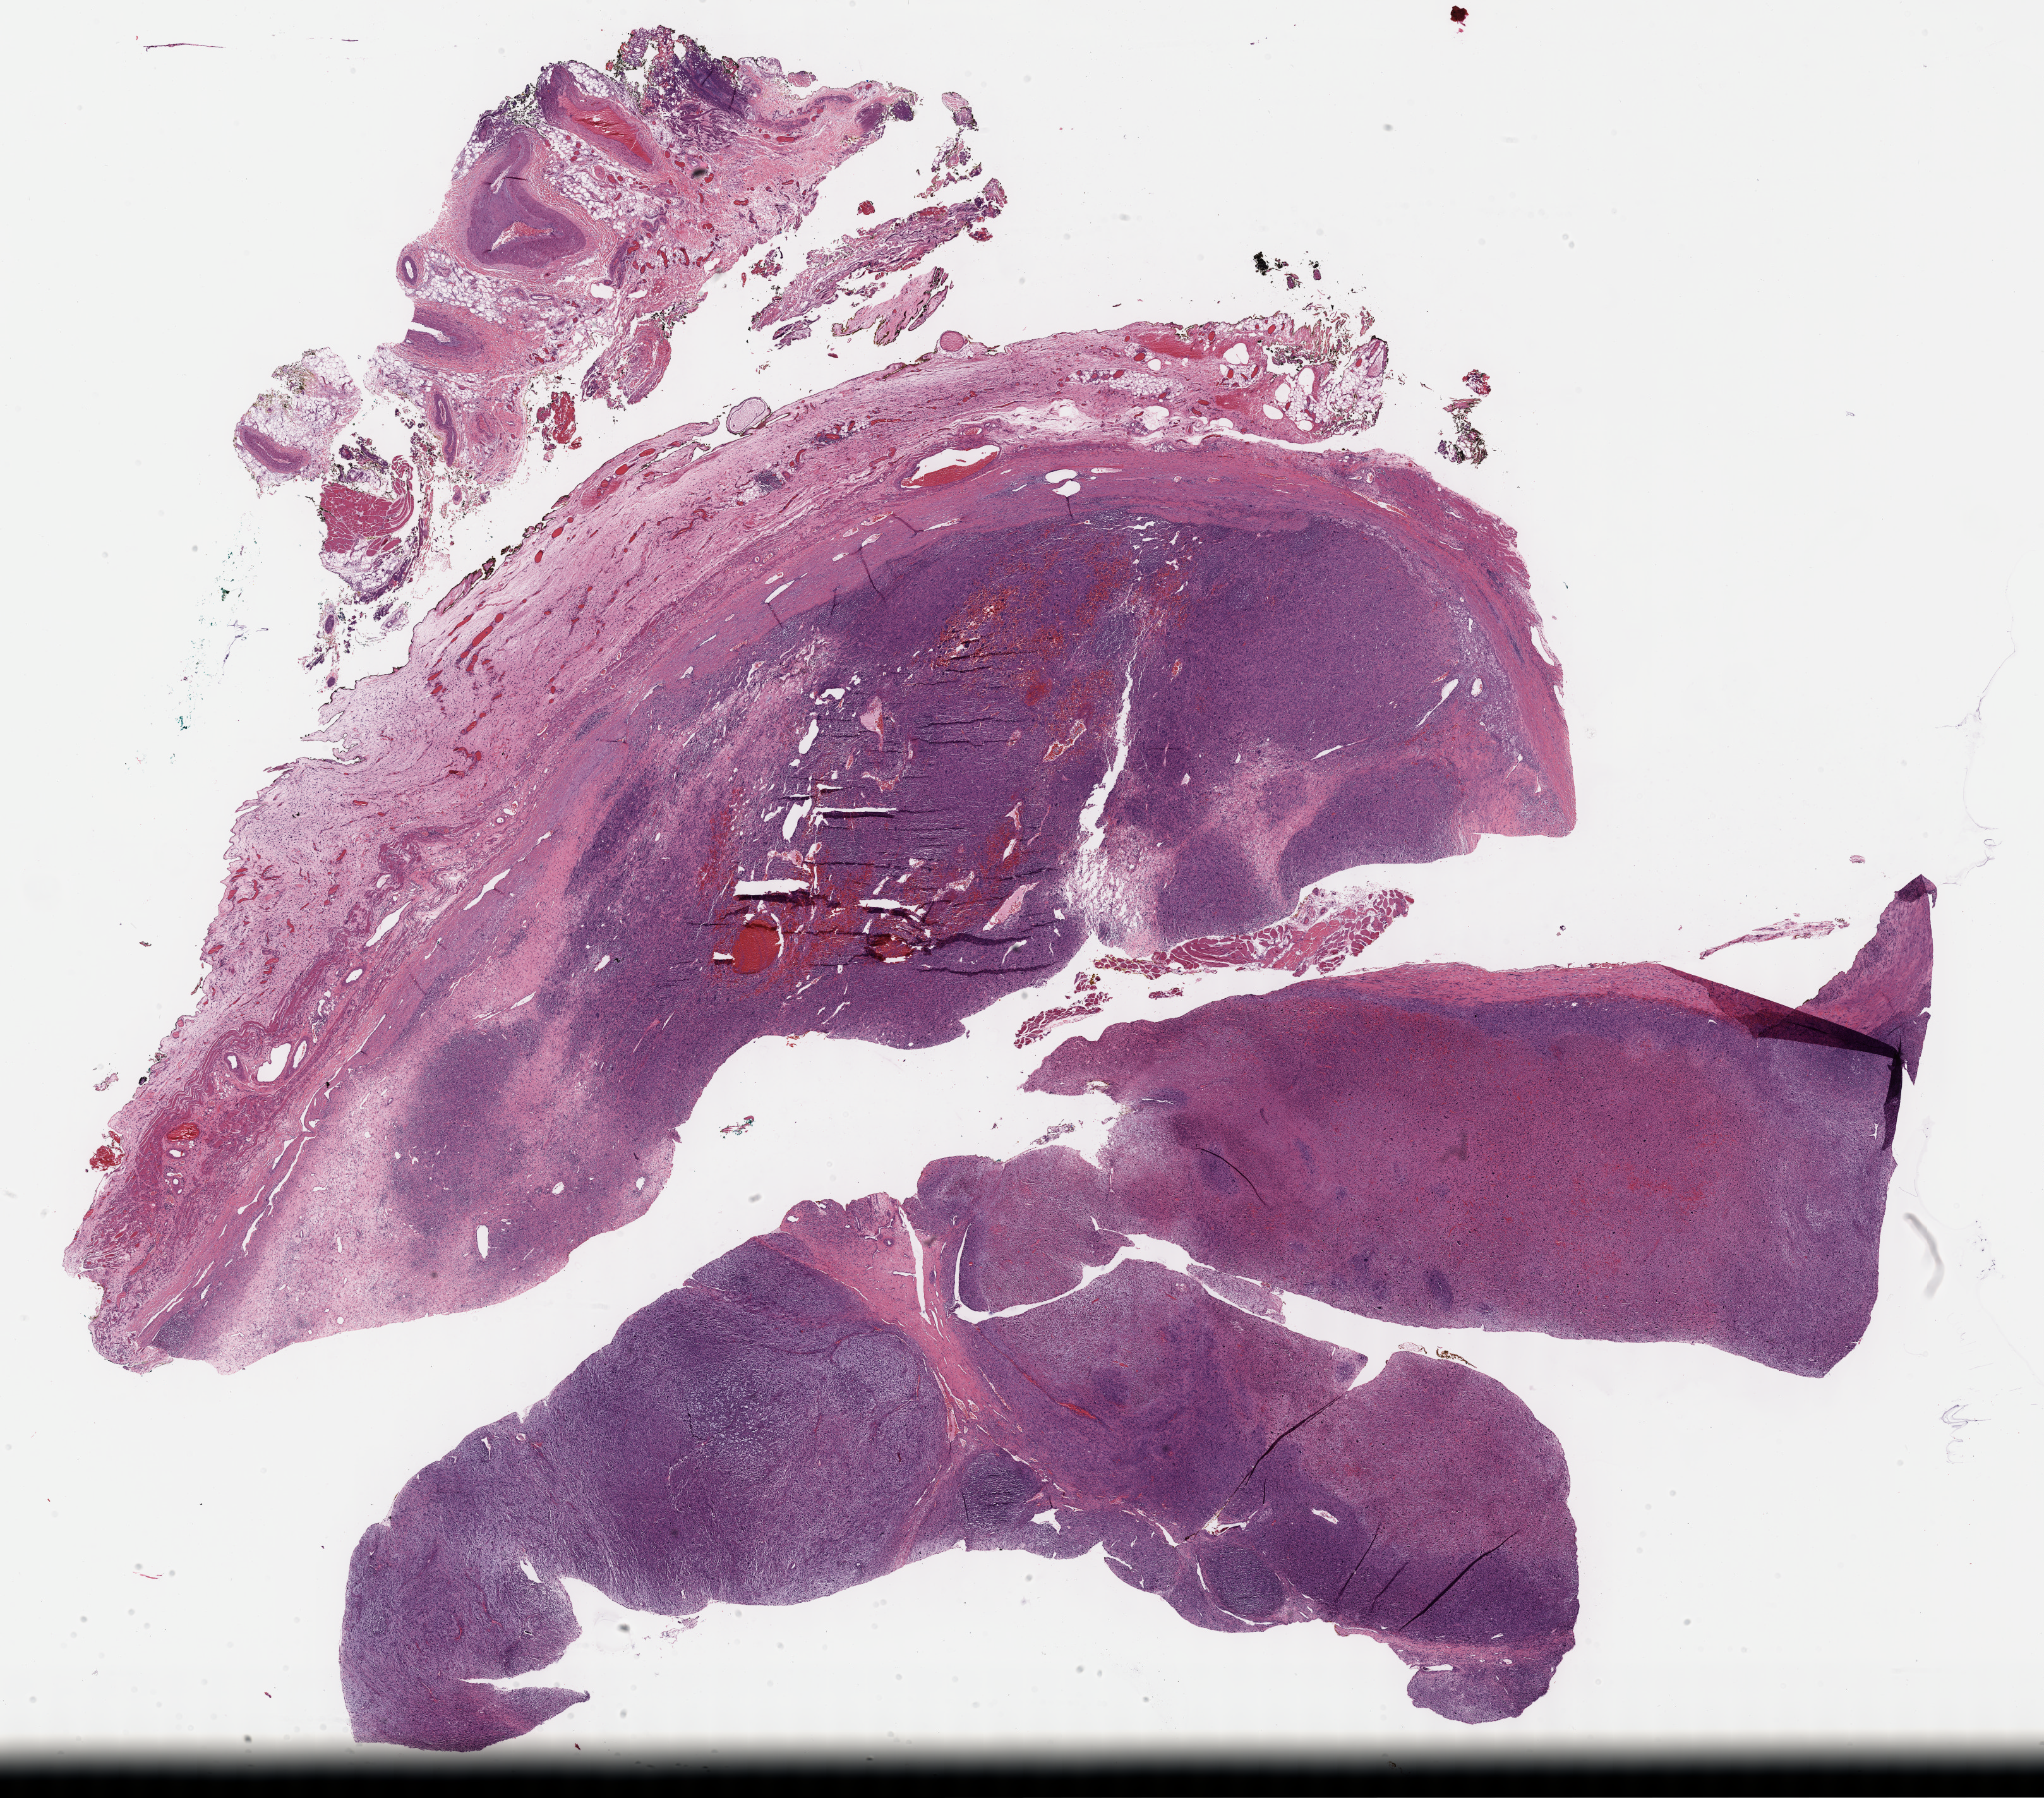
Whole-slide histology image, H&E-stained, a low-resolution overview of the entire scanned area, about 26.2 x 23.0 mm. Formalin-fixed paraffin-embedded (FFPE) diagnostic section. Connective, subcutaneous and other soft tissues, primary tumour sample. Patient: male, age at initial diagnosis 51 years.
Pathologic diagnosis: Fibromyxosarcoma (connective, subcutaneous and other soft tissues of thorax).